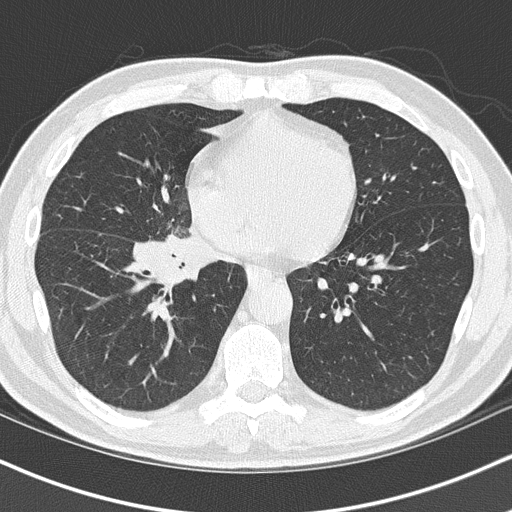
Low-dose screening chest CT, one axial slice; position 52 of 151 along the scan axis; 120 kVp; lung window (W 1500 / L -600 HU); 2 mm slice thickness; 512 × 512 image matrix, field of view 320 × 320 mm.
Structures marked on this image (outlined manually by an expert reader):
- lesion 1 (tumor, hilum of right lung): bounding box [x1, y1, x2, y2] px = [137, 234, 211, 282]